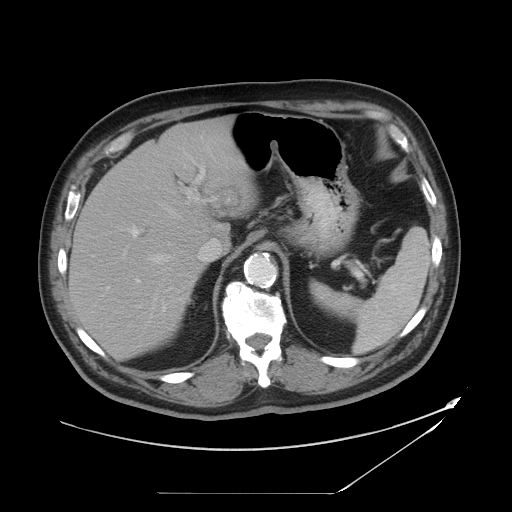
Contrast-enhanced abdominal CT, one axial slice; slice 32 of 49 in the series (ordered by position); 120 kVp; intravenous contrast given; soft-tissue window (W 400 / L 40 HU); 5 mm slice thickness; 512 × 512 image matrix. Male patient, age 72 years. Case-level facts recorded for this patient, not image findings: diagnosis: colorectal cancer liver metastases, imaged before liver resection; multiple liver metastases: no; largest metastasis: 2.5 cm.
Outlined on this slice (expert manual segmentation):
- hepatic veins: box from (x=146, y=186) to (x=218, y=269) px
- liver: (x=70, y=118)–(x=254, y=358)
- planned liver remnant (the part of the liver to remain after resection): (x=70, y=171)–(x=202, y=358)
- portal vein (with intrahepatic branches): (x=131, y=158)–(x=216, y=283)
- liver metastasis: (x=216, y=186)–(x=245, y=213)